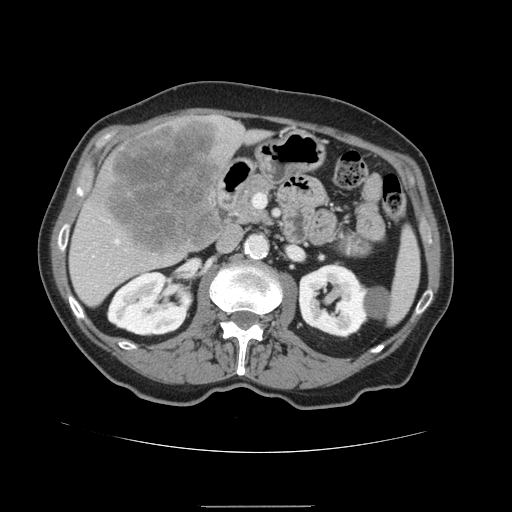
Contrast-enhanced abdominal CT, one axial slice. Soft-tissue window (W 400 / L 40 HU). 2.5 mm slice thickness. 512 × 512 image matrix, field of view 386 × 386 mm. Male patient, age 74 years. From the clinical record (not read from this slice): diagnosis: colorectal cancer liver metastases, imaged before liver resection.
Structures marked on this image (manually delineated by an expert):
- hepatic veins: bounding box <117,240,119,242> (left, top, right, bottom; pixels)
- liver: <68,115,271,308>
- planned liver remnant (the part of the liver to remain after resection): <71,131,271,308>
- liver metastasis: <105,119,223,254>